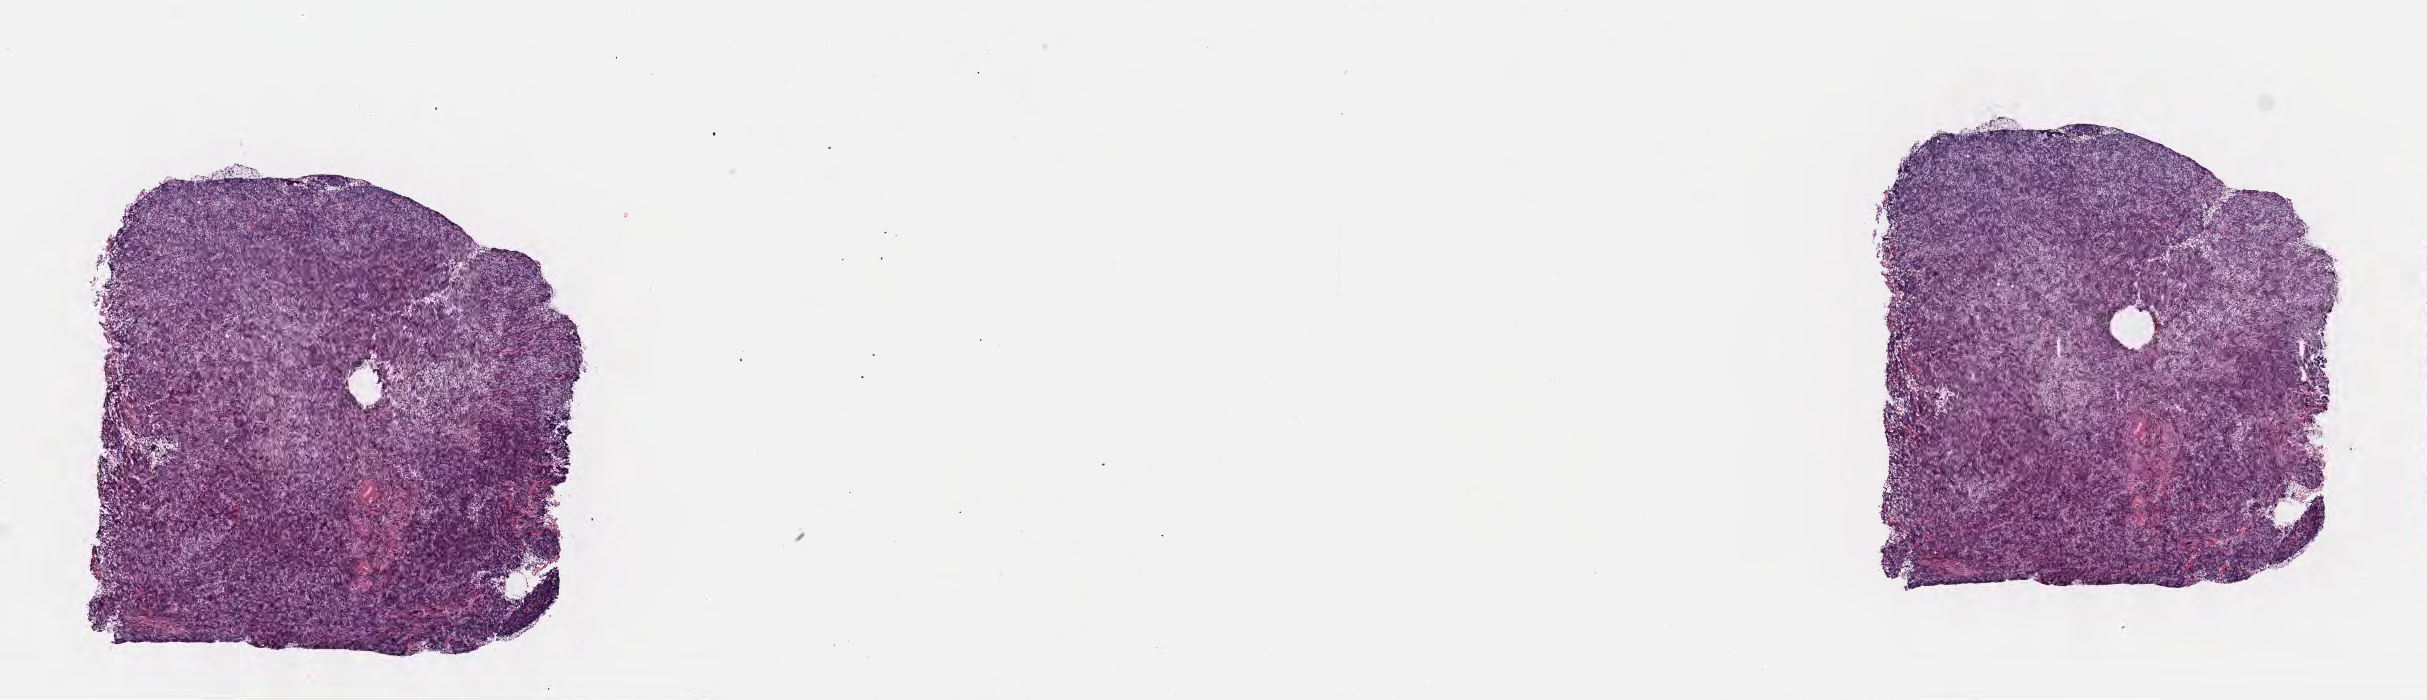
Digitized H&E-stained section, a low-resolution overview of the entire scanned area, about 19.6 x 5.7 mm. Cryosection. Specimen: primary tumor. Anatomic site: cranium. Patient: male, age at initial diagnosis 8 years.
Histologic diagnosis: Burkitt lymphoma, NOS.